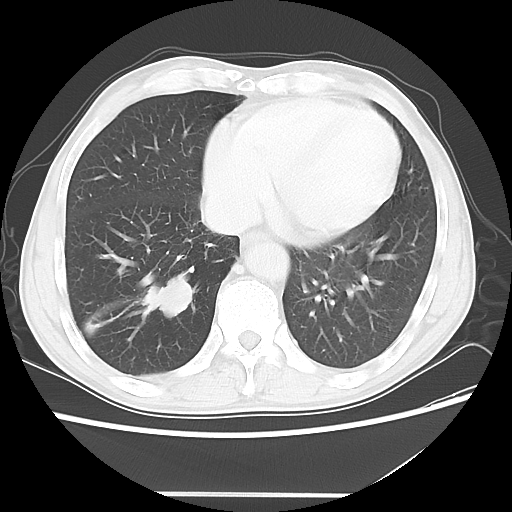
Chest CT, one axial slice. Position 16 of 56 along the scan axis. Reconstruction kernel LUNG. Lung window (W 1500 / L -600 HU). 5 mm slice thickness. 512 × 512 image matrix, field of view 344 × 344 mm. Patient: male, 65 years. Case-level facts recorded for this patient, not image findings: clinical TNM (as recorded): T1c N3 M0.
Annotated regions visible in this slice (bounding box drawn by a radiologist):
- lung tumour (recorded histology: small cell carcinoma): bounding box (x1, y1, x2, y2) in pixels: (142, 268, 200, 322)